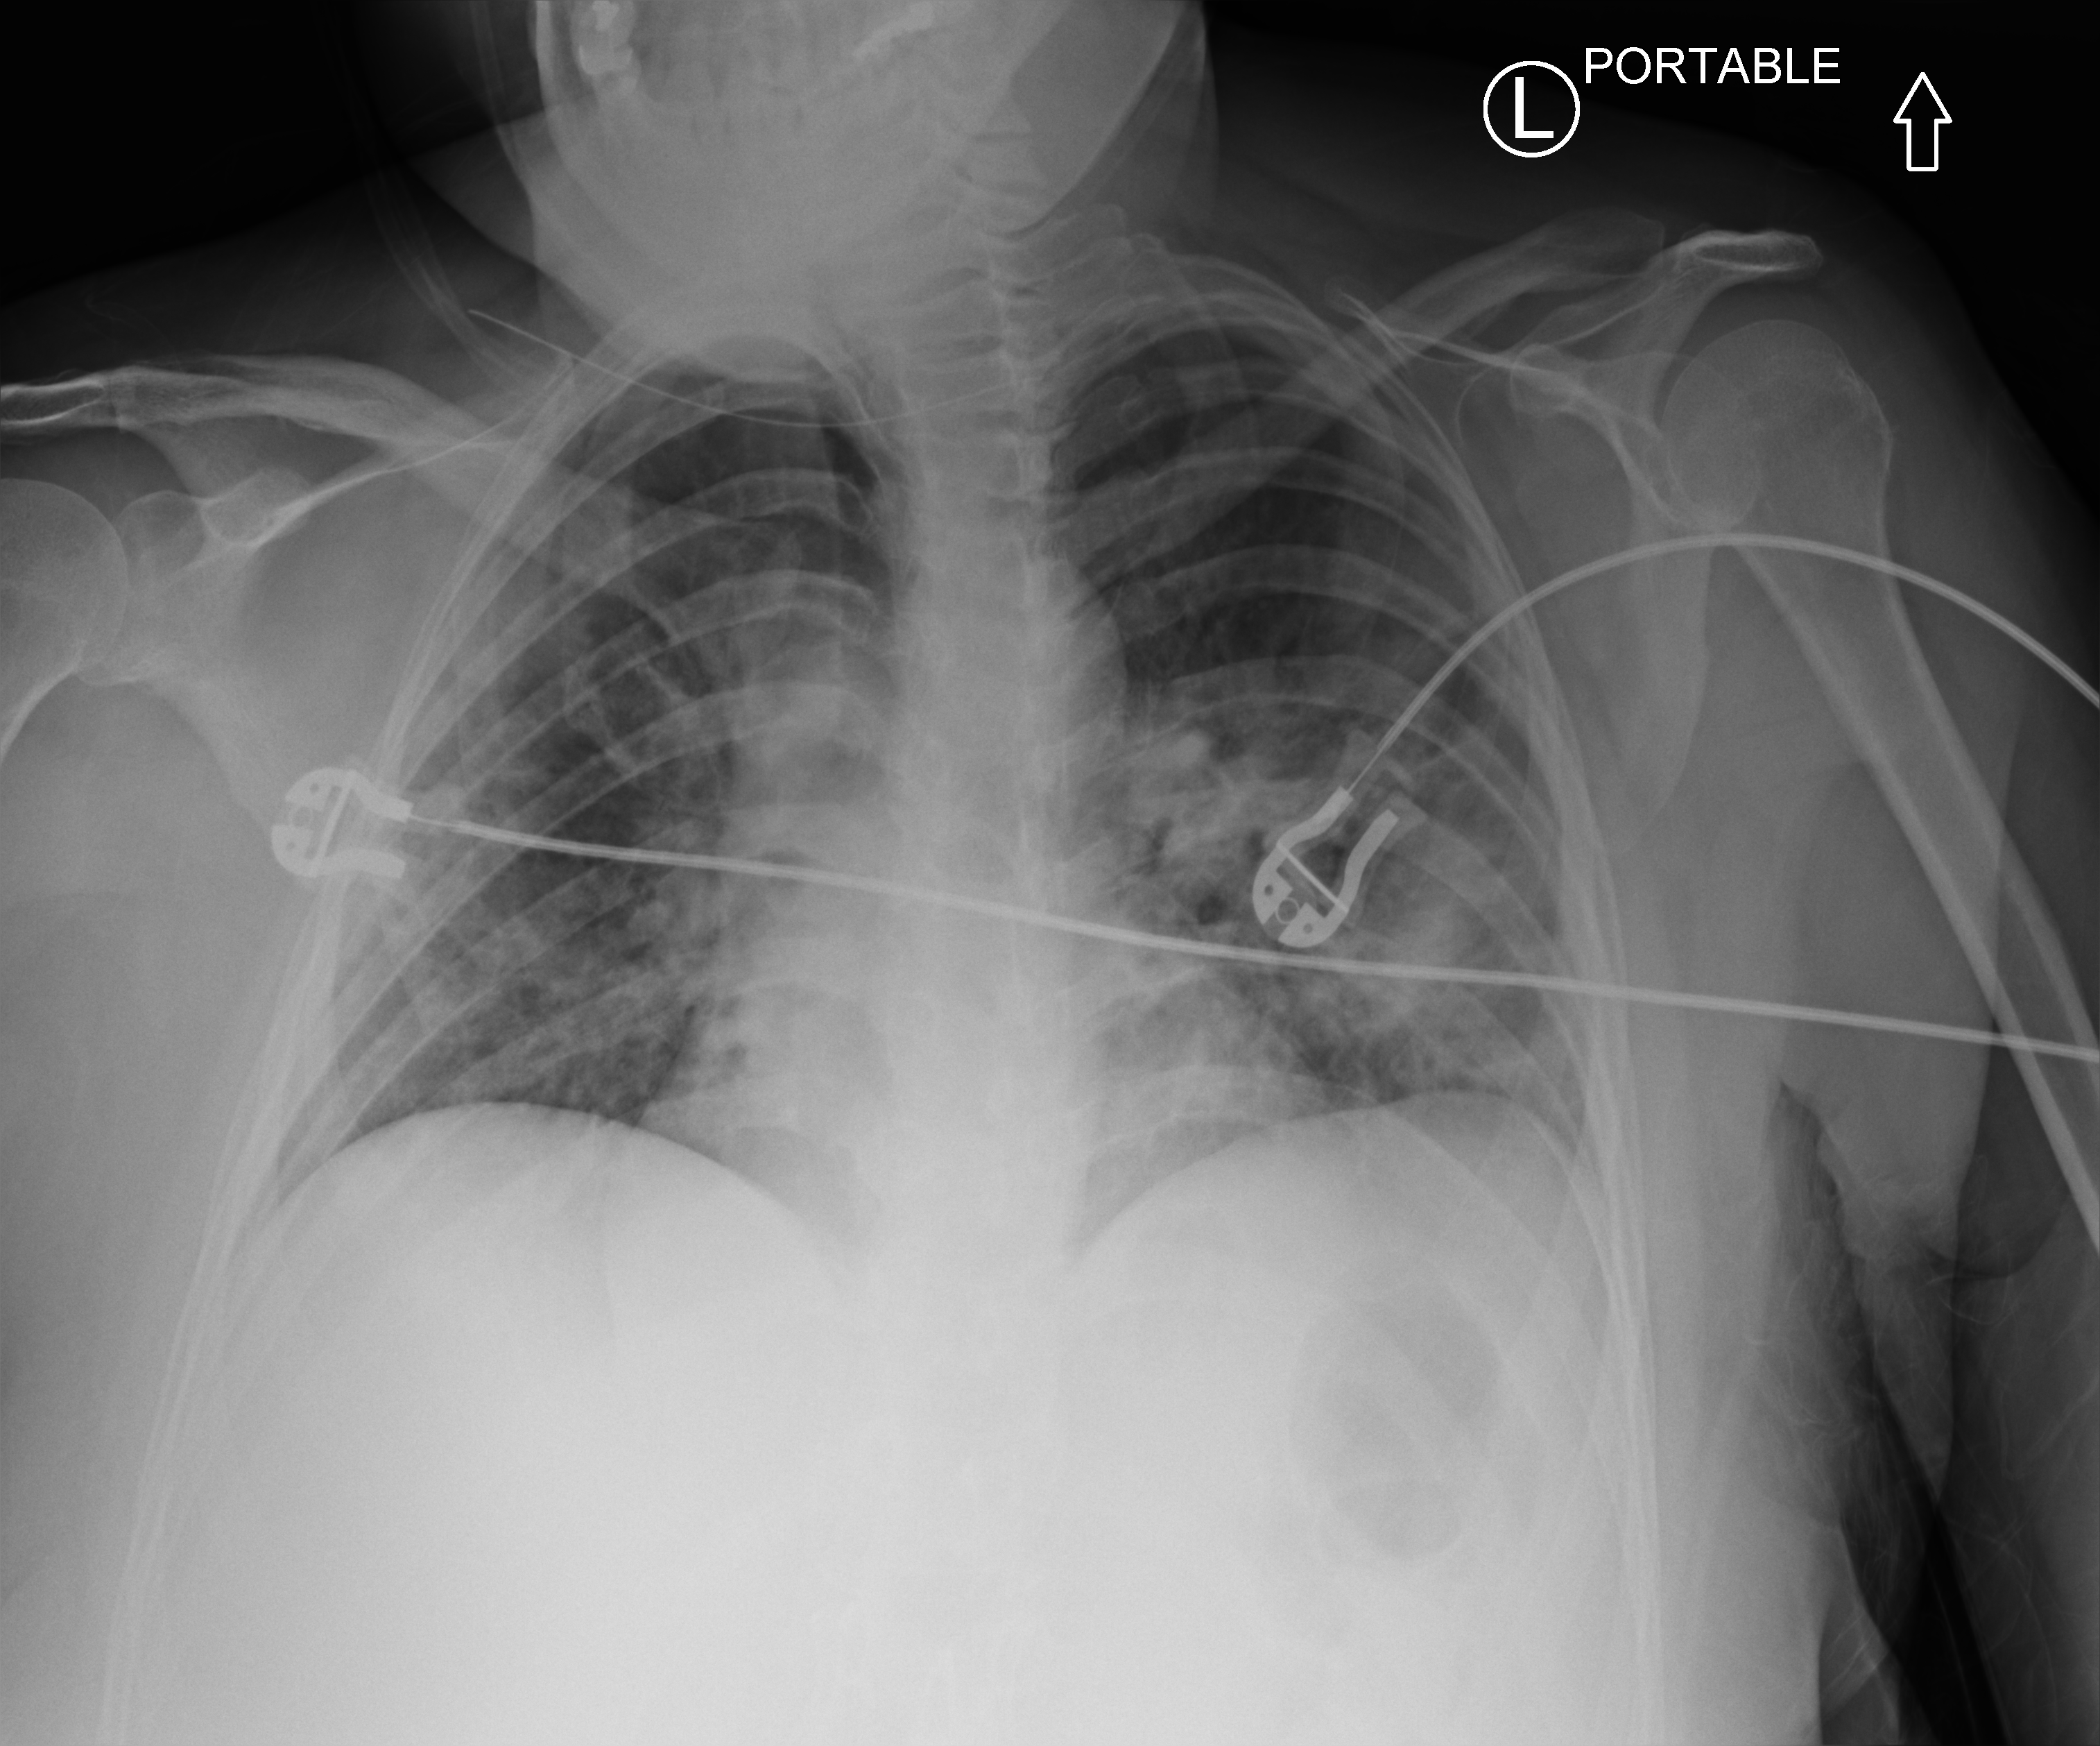
Bedside chest radiograph (computed radiography), anteroposterior (AP) projection. Female patient hospitalised with COVID-19, age 18–59 years.
Admission-level facts for this patient (not findings on this image; timing relative to this image not recorded): hypertension (admission record): no.